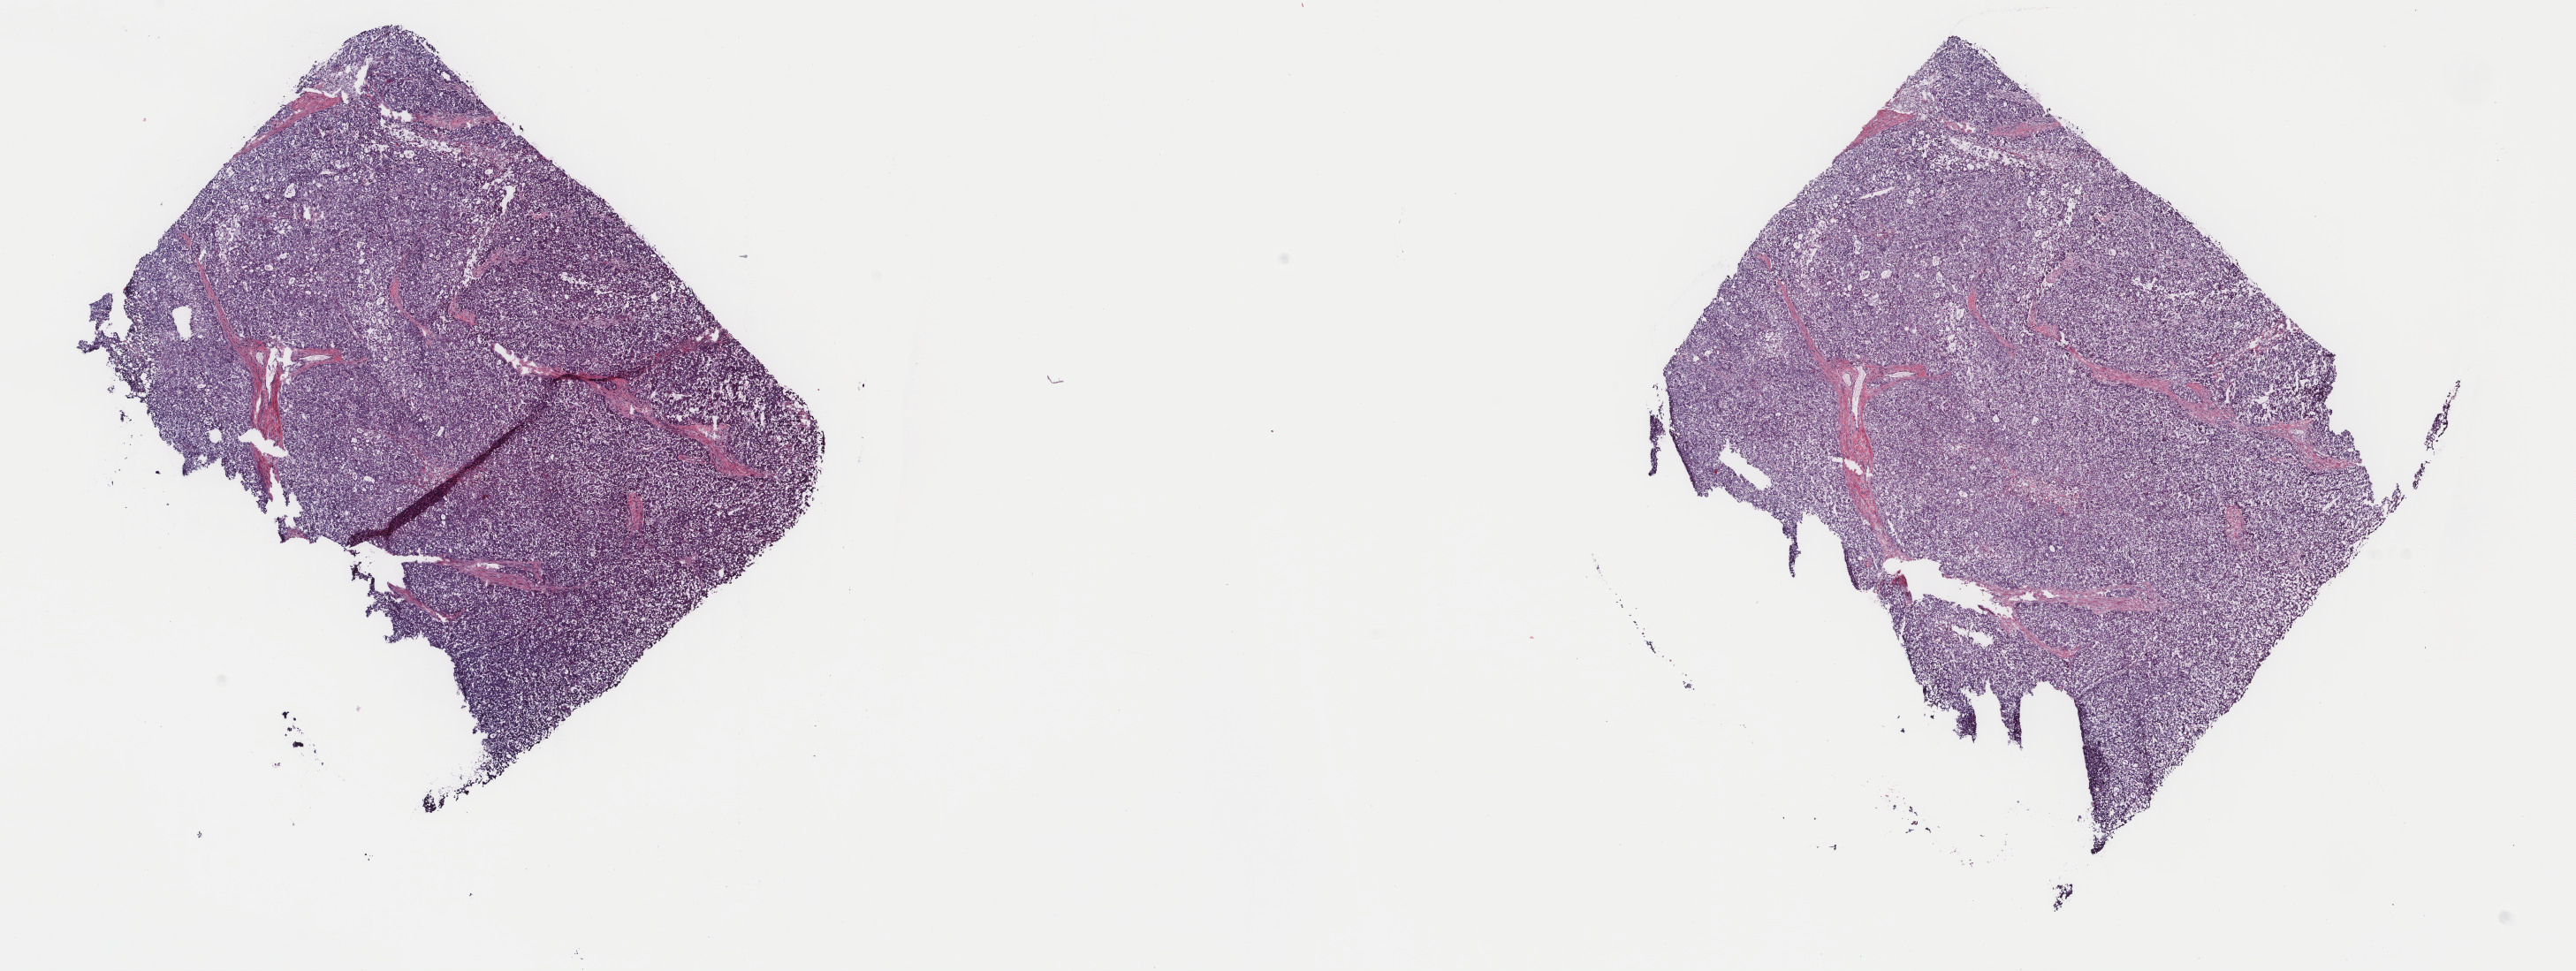
Whole-slide histology image, H&E, shown as a low-resolution overview of the whole scanned area (about 23.1 x 8.7 mm, from a 40x scan); frozen section from the top of the tissue portion; primary tumour sample from the liver. Female, age 67 years at initial diagnosis. Histologic grade: G3 (poorly differentiated). Pathologist review of this section (percent, as recorded): tumour cells 100%, tumour nuclei 80%, normal cells 0%, stromal cells 0%, necrosis 0%. Inflammatory infiltration, as recorded: lymphocyte infiltration 1%, monocyte infiltration 0%, neutrophil infiltration 0%.
• diagnosis: Hepatocellular carcinoma, NOS
• AJCC pathologic stage: IIIC (6th edition)
• TNM: T2 N1 M0